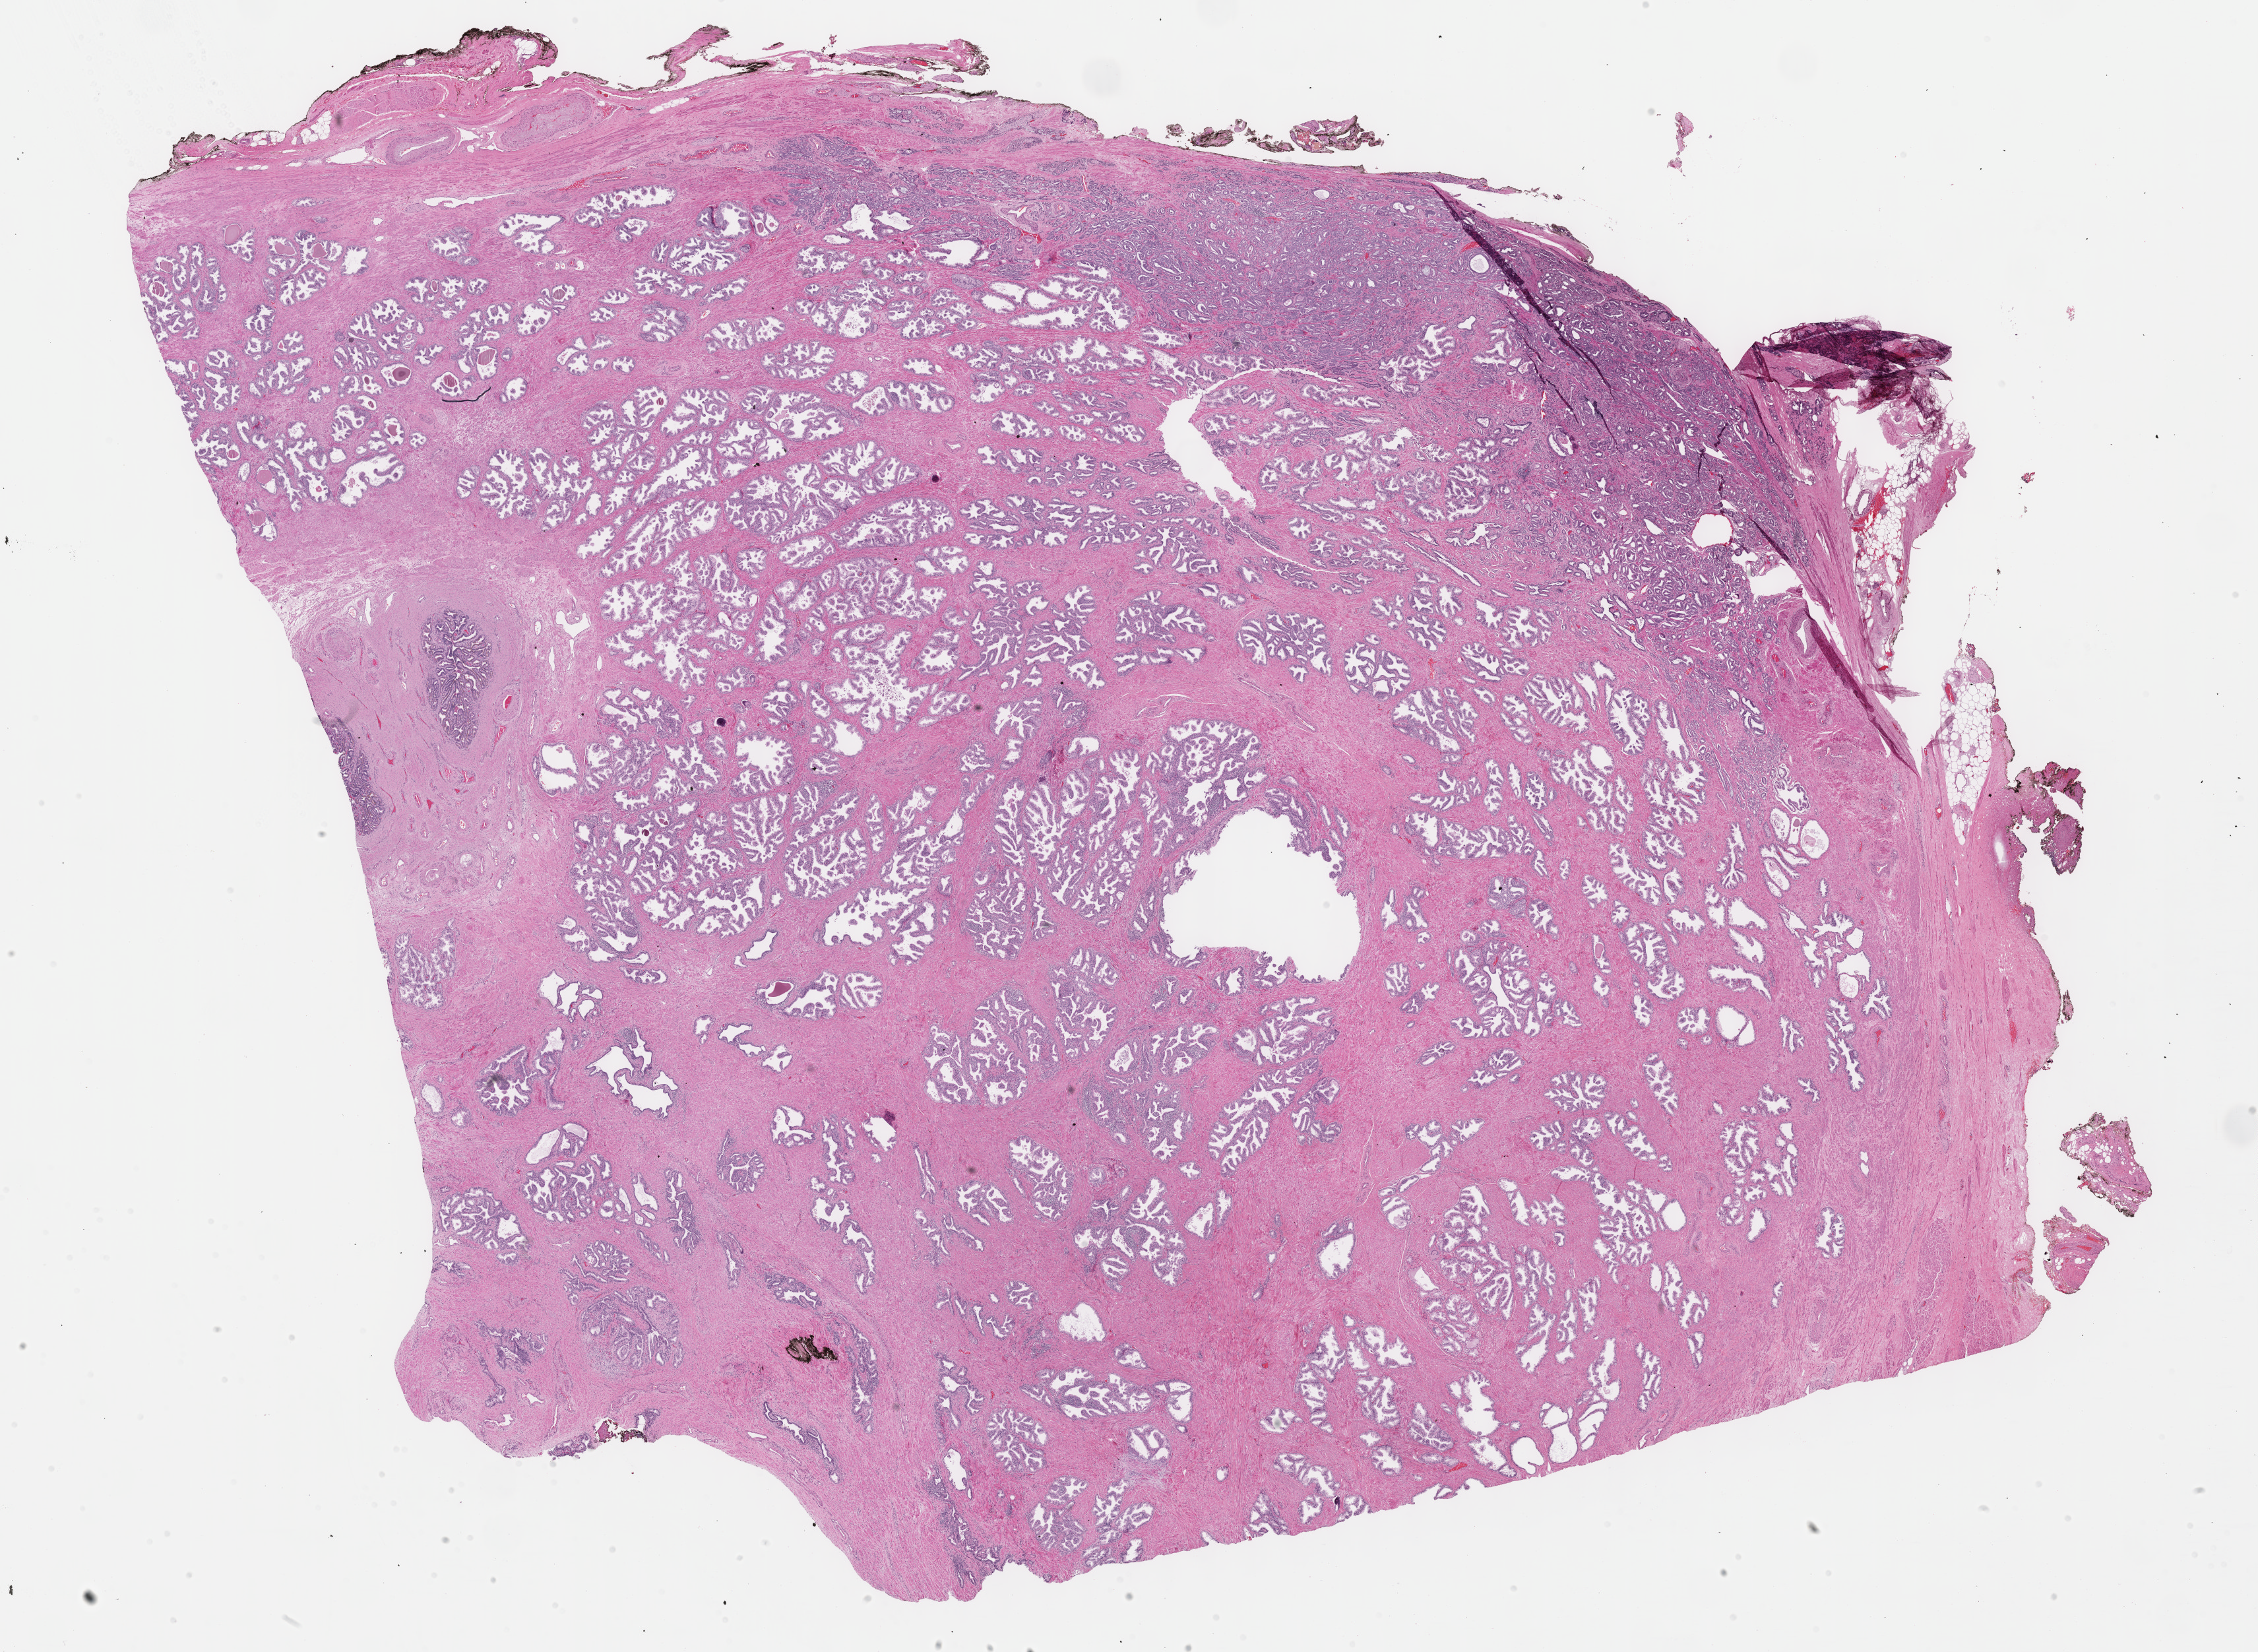
H&E-stained whole-slide image, a low-resolution overview of the entire scanned area, about 27.7 x 20.3 mm, formalin-fixed paraffin-embedded (FFPE) diagnostic section, primary tumour sample from the prostate. Patient: male, age at initial diagnosis 48 years. Gleason score: 6 (3+3).
* diagnosis: Adenocarcinoma, NOS (prostate gland)
* laterality: right